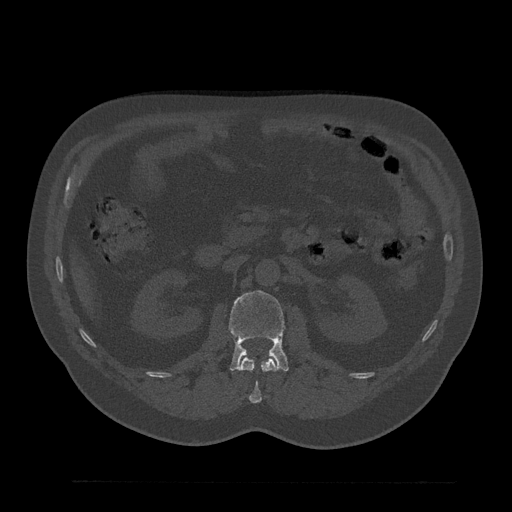
CT including the spine, one axial slice. Position 125 of 797 along the scan axis. Bone window (W 1800 / L 400 HU). 0.5 mm slice thickness. 512 × 512 image matrix, field of view 430 × 430 mm. Patient: male, 61 years. From the clinical record (not read from this slice): primary cancer: prostate.
Outlined on this slice (semi-automatically segmented with operator editing):
- L1 vertebra: bounding box <240,357,278,403> (left, top, right, bottom; pixels)
- L2 vertebra: <229,291,289,371>